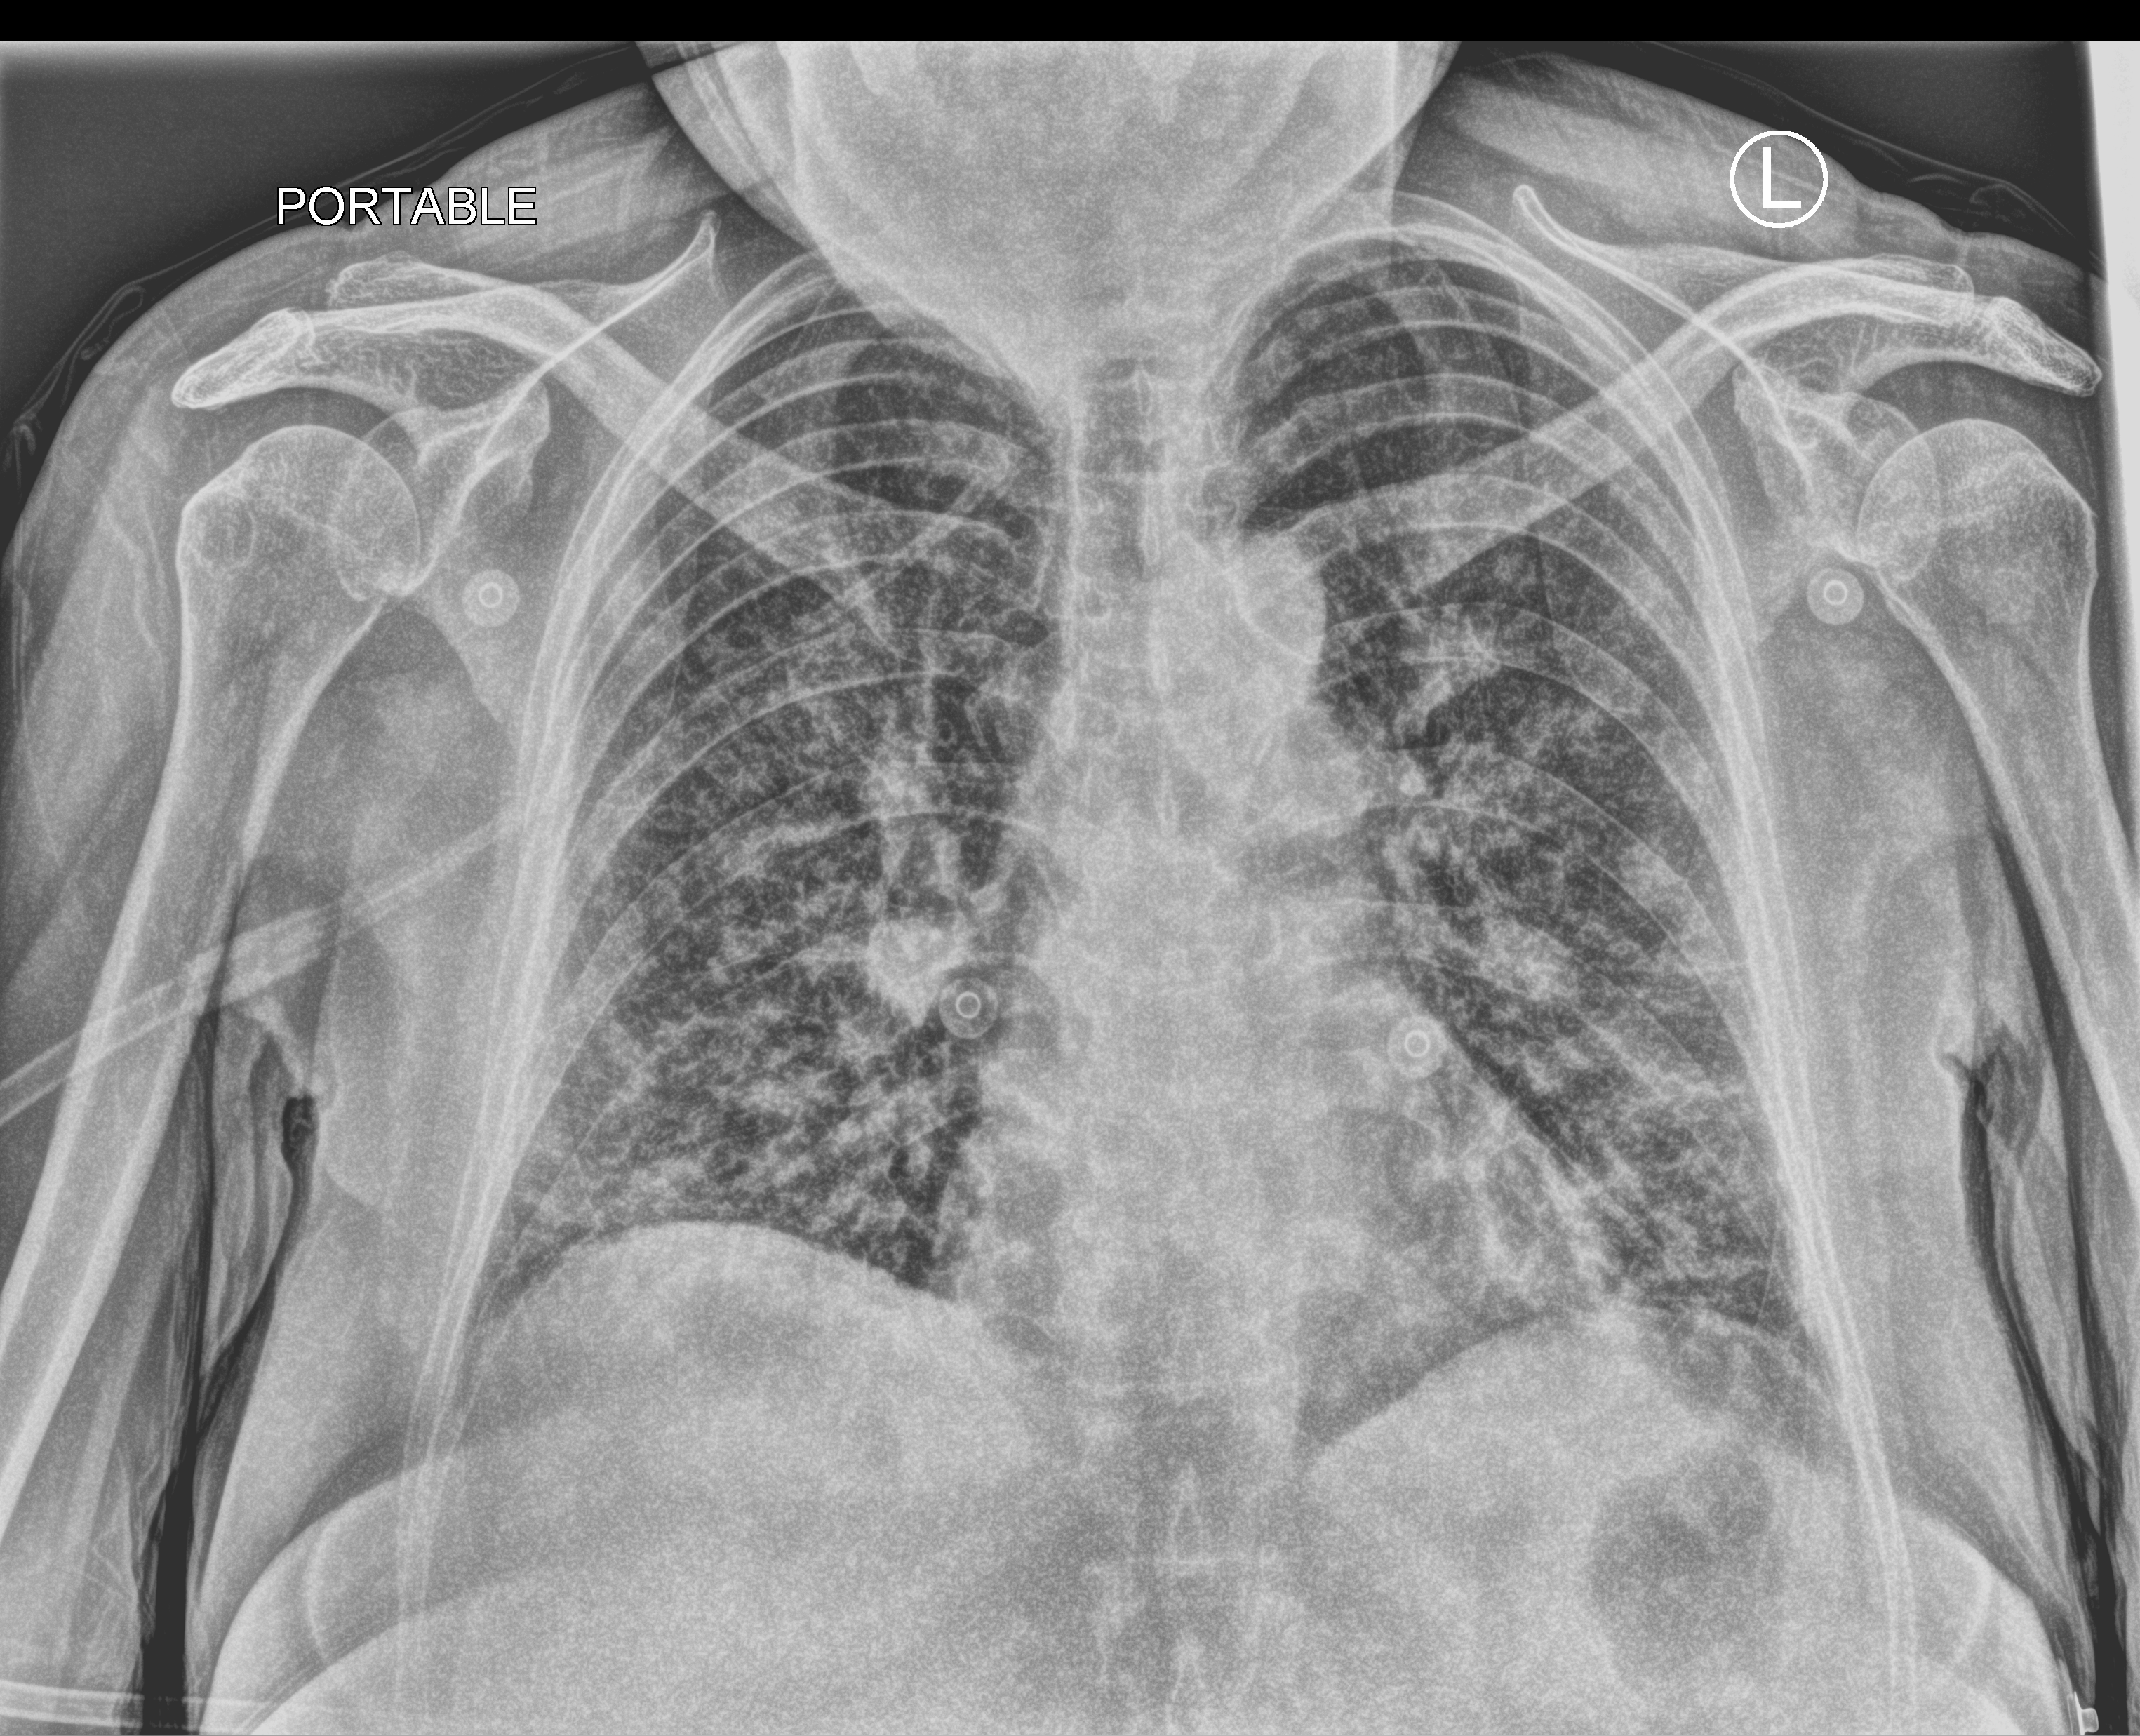
Portable chest radiograph; anteroposterior (AP) projection. Patient hospitalised with COVID-19; female, aged 60–74 years.
Hospital-stay facts (about this admission, not read from this image; timing relative to this image not recorded): mechanically ventilated during this hospital stay: no; admitted to intensive care during this hospital stay: no.